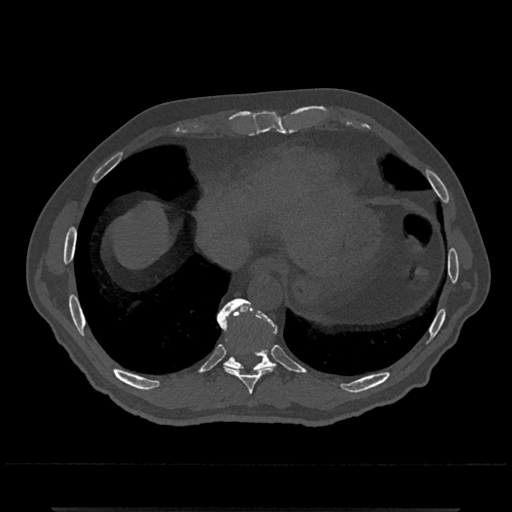
CT including the spine, one axial slice; slice 588 of 797 in the series (ordered by position); reconstruction kernel Br40s/3; bone window (W 1800 / L 400 HU); 0.5 mm slice thickness; 512 × 512 image matrix, field of view 393 × 393 mm. Patient: male, 67 years. Case-level facts recorded for this patient, not image findings: primary cancer: prostate.
Outlined on this slice (semi-automatically segmented with operator editing):
- T10 vertebra: box from (x=218, y=298) to (x=276, y=372) px
- T9 vertebra: (x=218, y=310)–(x=276, y=394)